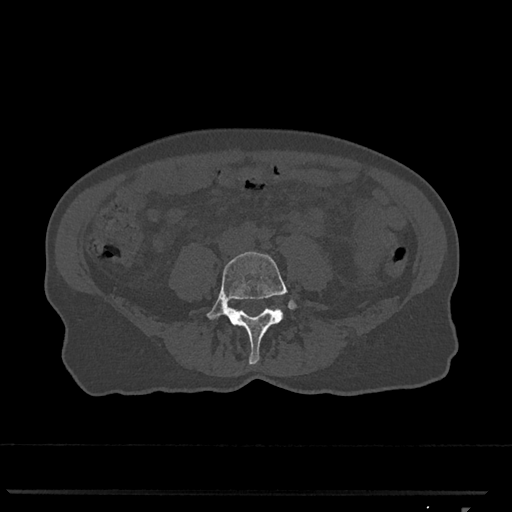
CT including the spine, one axial slice. Slice 206 of 793 in the series (ordered by position). Reconstruction kernel Br40s/3. 120 kVp. Bone window (W 1800 / L 400 HU). 512 × 512 image matrix, field of view 380 × 380 mm. Female patient, age 62 years. From the clinical record (not read from this slice): primary cancer: renal.
Structures marked on this image (semi-automatic segmentation, software-assisted and operator-edited):
- L4 vertebra: bounding box <206,251,297,365> (left, top, right, bottom; pixels)